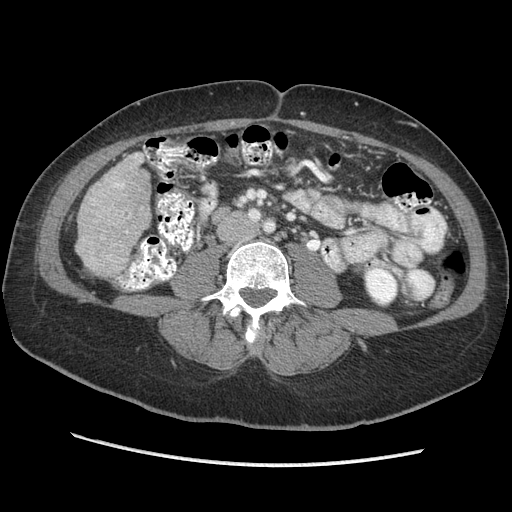
Contrast-enhanced abdominal CT (liver protocol), one axial slice; position 89 of 170 along the scan axis; reconstruction kernel STANDARD; 140 kVp; soft-tissue window (W 400 / L 40 HU); 2.5 mm slice thickness; 512 × 512 image matrix, field of view 360 × 360 mm. From the clinical record (not read from this slice): diagnosis: hepatocellular carcinoma (patient treated with transarterial chemoembolisation; whether this scan precedes or follows treatment is not stated here); TNM stage (as recorded): Stage-II; Child-Pugh class: A; tumour nodularity: multinodular; tumour size: 4 cm.
Structures marked on this image (semi-automatic segmentation, software-assisted and operator-edited):
- liver parenchyma outside the tumour (the mass and vessels are separate outlines, so this box may not span the whole liver): bounding box (x1, y1, x2, y2) in pixels: (76, 151, 150, 276)
- liver vessels: (115, 155, 137, 188)